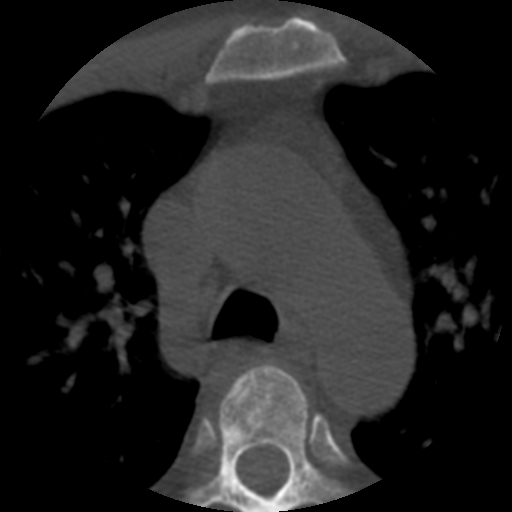
CT including the spine, one axial slice; slice 397 of 508 in the series (ordered by position); 120 kVp; bone window (W 1800 / L 400 HU); 1.25 mm slice thickness; 512 × 512 image matrix, field of view 160 × 160 mm. Patient age 57 years. Case-level facts recorded for this patient, not image findings: primary cancer: prostate.
Structures marked on this image (semi-automatically segmented with operator editing):
- T3 vertebra: box from (x=222, y=364) to (x=300, y=408) px
- T4 vertebra: (x=190, y=377)–(x=347, y=512)
- T5 vertebra: (x=239, y=480)–(x=244, y=485)